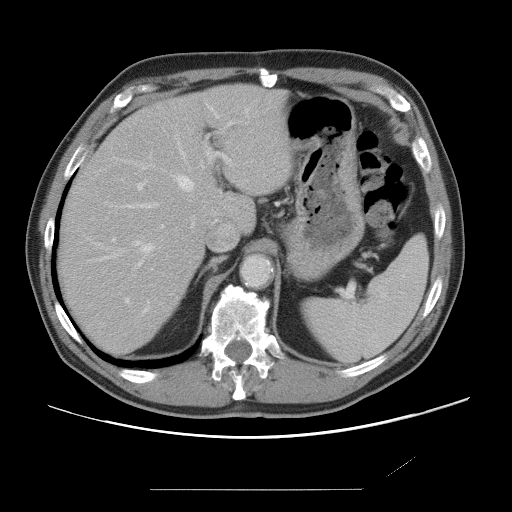
Contrast-enhanced abdominal CT, one axial slice; position 52 of 87 along the scan axis; soft-tissue window (W 400 / L 40 HU); 512 × 512 image matrix. Male patient, age 74 years. From the clinical record (not read from this slice): diagnosis: colorectal cancer liver metastases, imaged before liver resection; multiple liver metastases: yes.
Annotated regions visible in this slice (expert manual segmentation):
- hepatic veins: box from (x=102, y=109) to (x=248, y=312) px
- liver: (x=60, y=86)–(x=291, y=354)
- planned liver remnant (the part of the liver to remain after resection): (x=60, y=86)–(x=291, y=354)
- portal vein (with intrahepatic branches): (x=112, y=122)–(x=233, y=303)